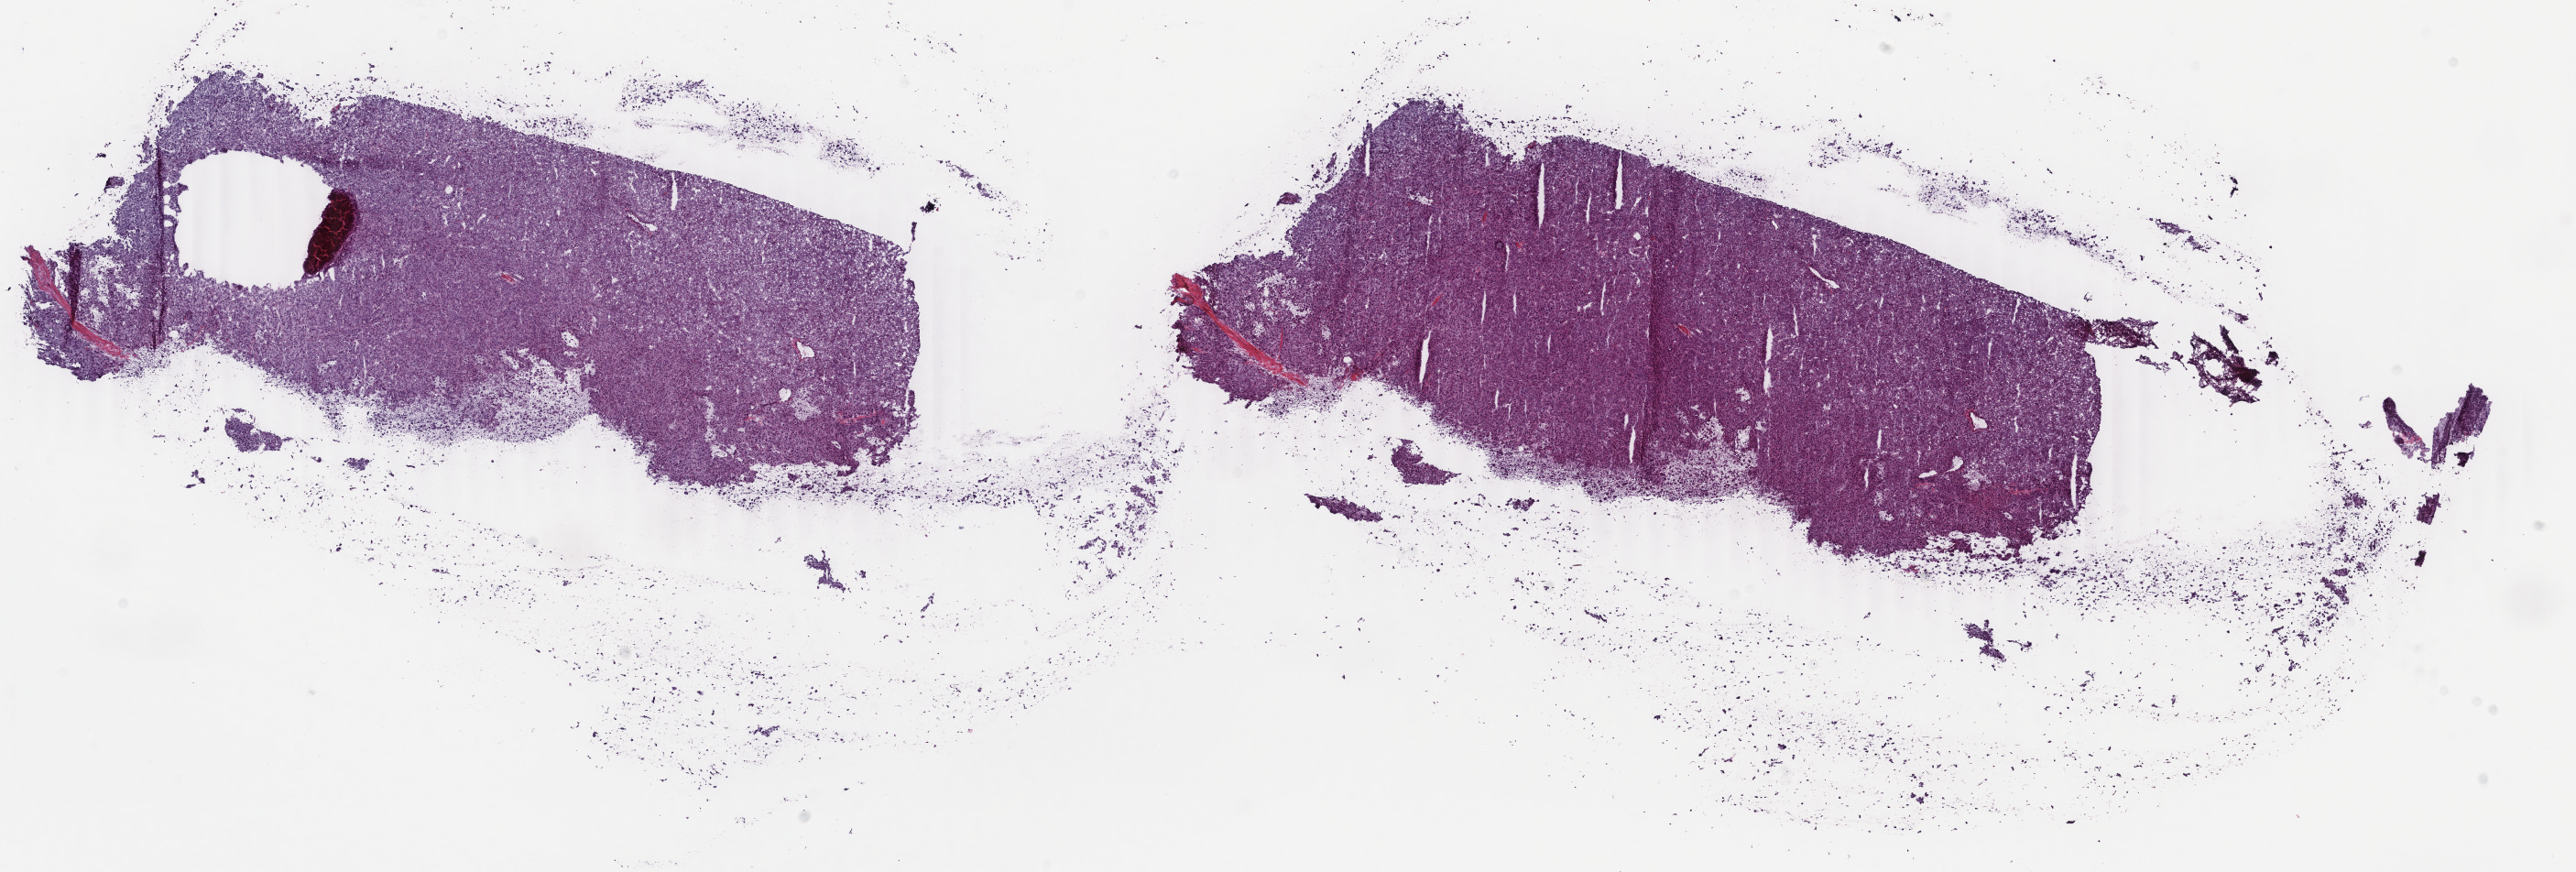
Digitized H&E-stained tissue section (whole slide) — a low-resolution overview of the entire scanned area, about 22.4 x 7.6 mm; frozen section from the top of the tissue portion; sample: primary tumour, liver. Female, age 77 years at initial diagnosis. Histologic grade: G2 (moderately differentiated). Slide review estimates, as recorded: tumour cells 95%, tumour nuclei 95%, normal cells 0%, stromal cells 5%, necrosis 0%. Inflammatory infiltration, as recorded: lymphocyte infiltration 1%, monocyte infiltration 0%, neutrophil infiltration 0%.
TNM: T2 N0 M0. Pathologic diagnosis: Hepatocellular carcinoma, NOS. AJCC pathologic stage: II (6th edition).